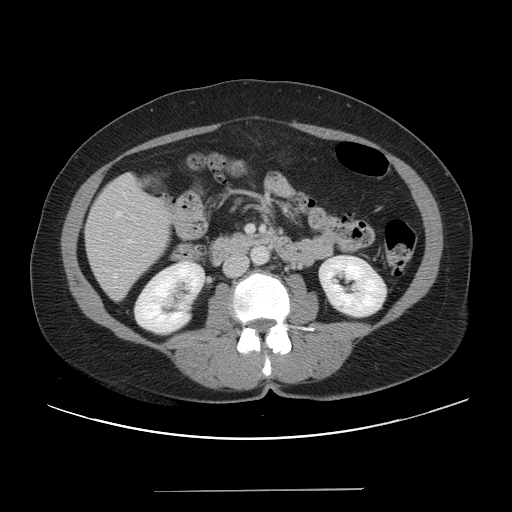
Contrast-enhanced abdominal CT, one axial slice. Slice 13 of 56 in the series (ordered by position). 120 kVp. Intravenous contrast given. Soft-tissue window (W 400 / L 40 HU). 512 × 512 image matrix, field of view 419 × 419 mm. Female patient, age 54 years. From the clinical record (not read from this slice): diagnosis: colorectal cancer liver metastases, imaged before liver resection; multiple liver metastases: yes; largest metastasis: 3.2 cm; disease in both lobes: yes.
Structures marked on this image (expert manual segmentation):
- liver: box from (x=87, y=174) to (x=170, y=299) px
- portal vein (with intrahepatic branches): (x=247, y=226)–(x=253, y=232)